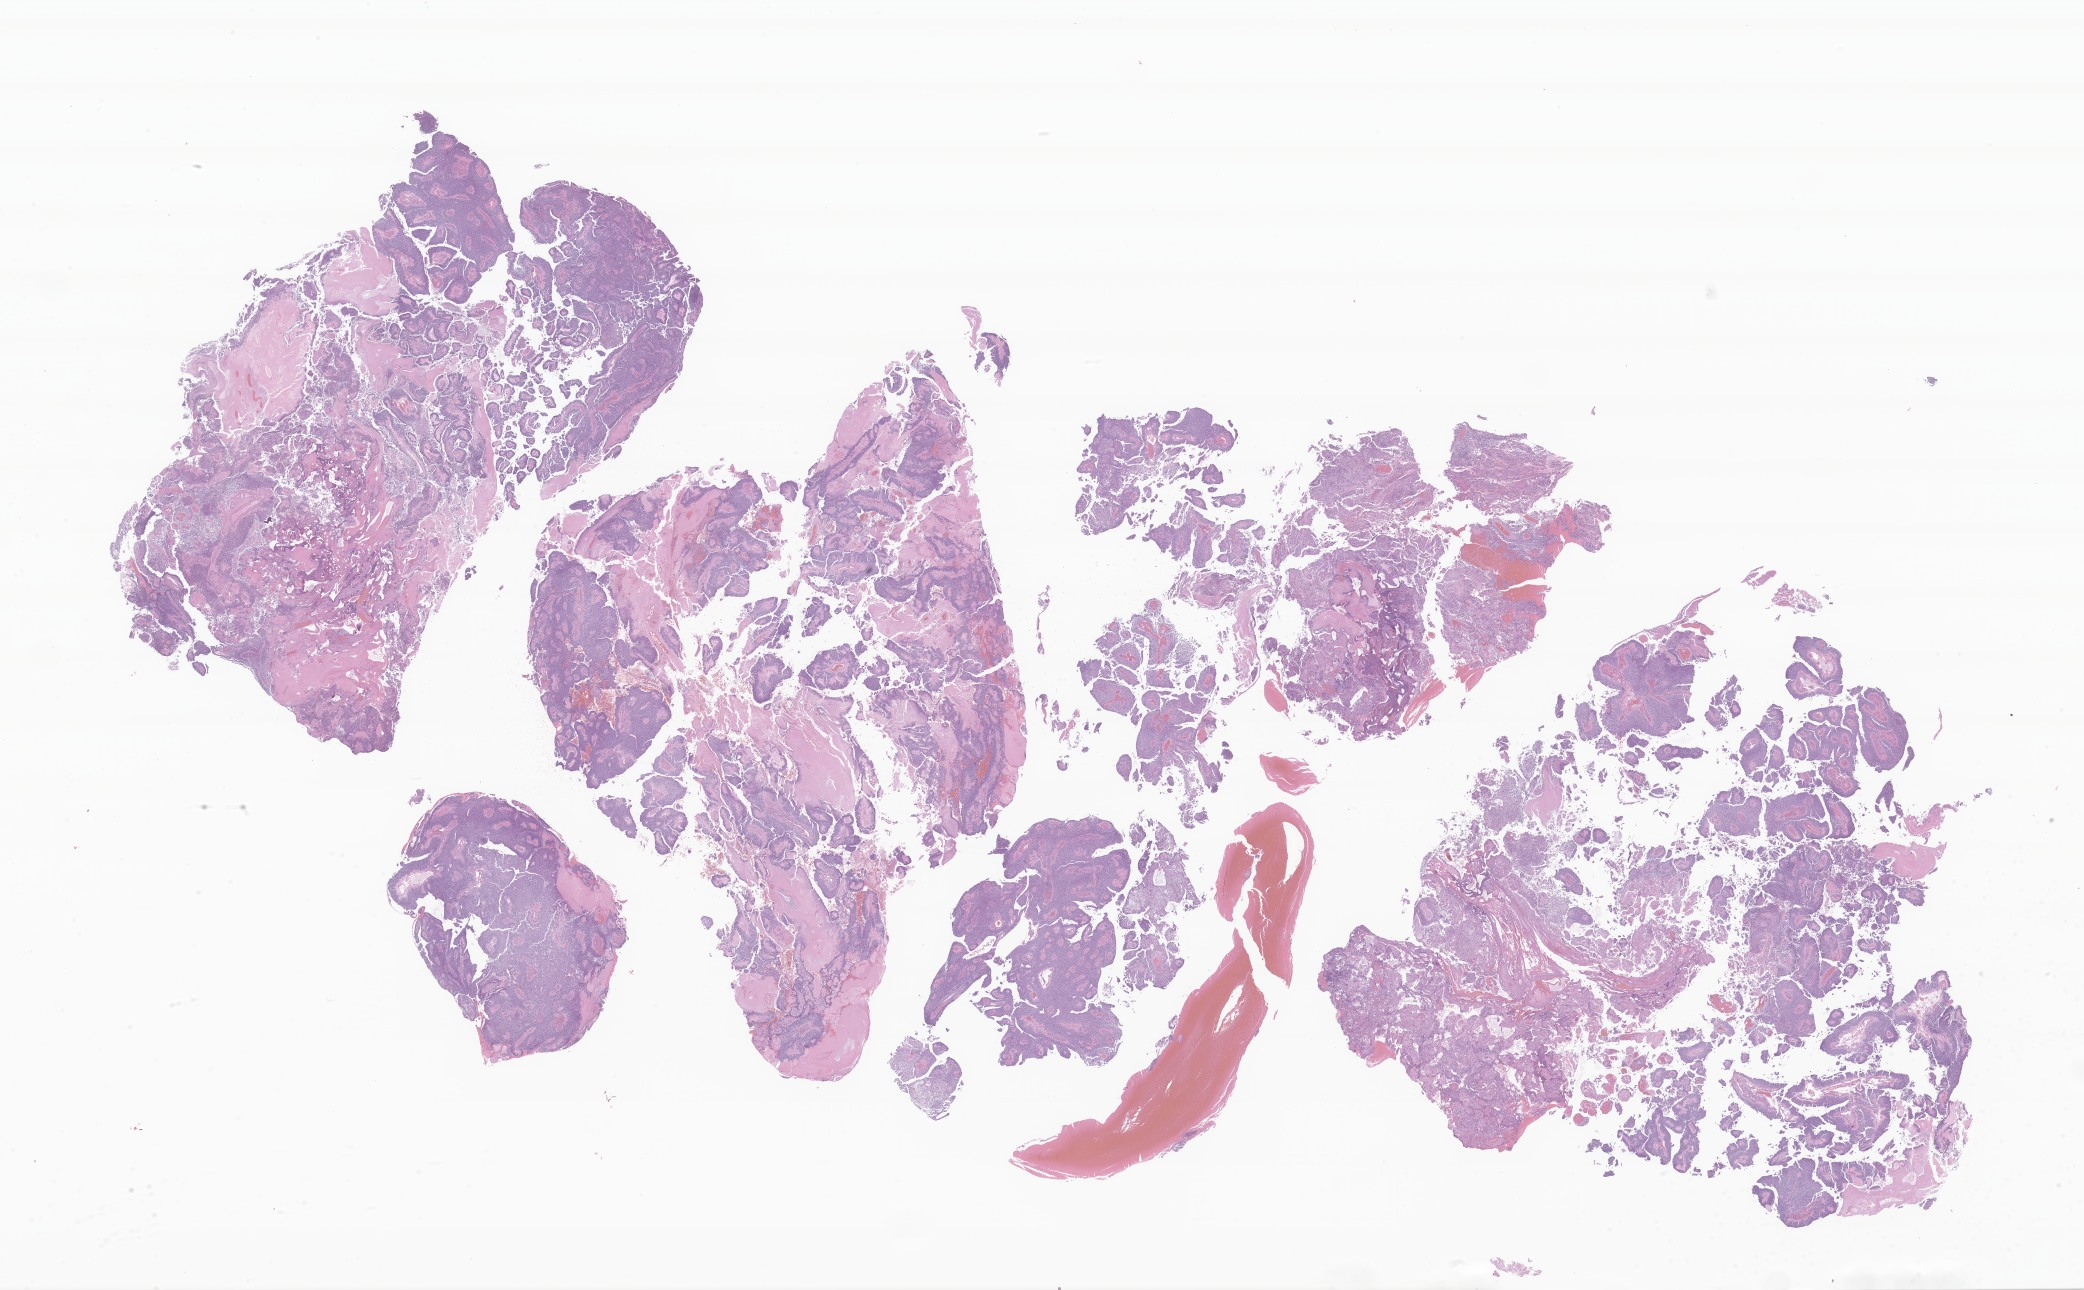
Digitized haematoxylin and eosin-stained section of tumor tissue from the brain — shown as a low-resolution overview of the whole scanned area (about 35.1 x 21.8 mm), formalin-fixed, paraffin-embedded (FFPE) tissue. Patient: male, age 766 days (about 2.1 years).
Diagnosis: Neoplasm, uncertain whether benign or malignant.